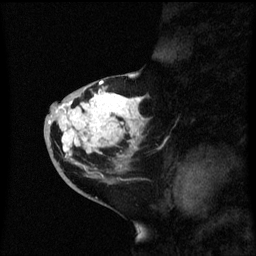
Breast MRI (dynamic contrast-enhanced), one sagittal slice; position 28 of 60 along the scan axis; dynamic contrast-enhanced series, image 2 of 3 at this slice position (ordered by acquisition); 1.5 T; TE 4.2 ms, TR 8.4 ms; 2.3 mm slice thickness; 256 × 256 image matrix, field of view 200 × 200 mm. Patient: female, 46 years. From the clinical record (not read from this slice): setting: breast cancer imaged before/during neoadjuvant chemotherapy; receptor status: HER2-positive.
Outlined on this slice (semi-automatically segmented with operator editing):
- analysis volume of interest (the breast-tissue region the enhancement analysis was run in; not a lesion): bounding box <44,86,151,171> (left, top, right, bottom; pixels)
- tumour enhancement mask (voxels above the 70 % enhancement threshold inside the analysis volume of interest): <48,90,145,157>